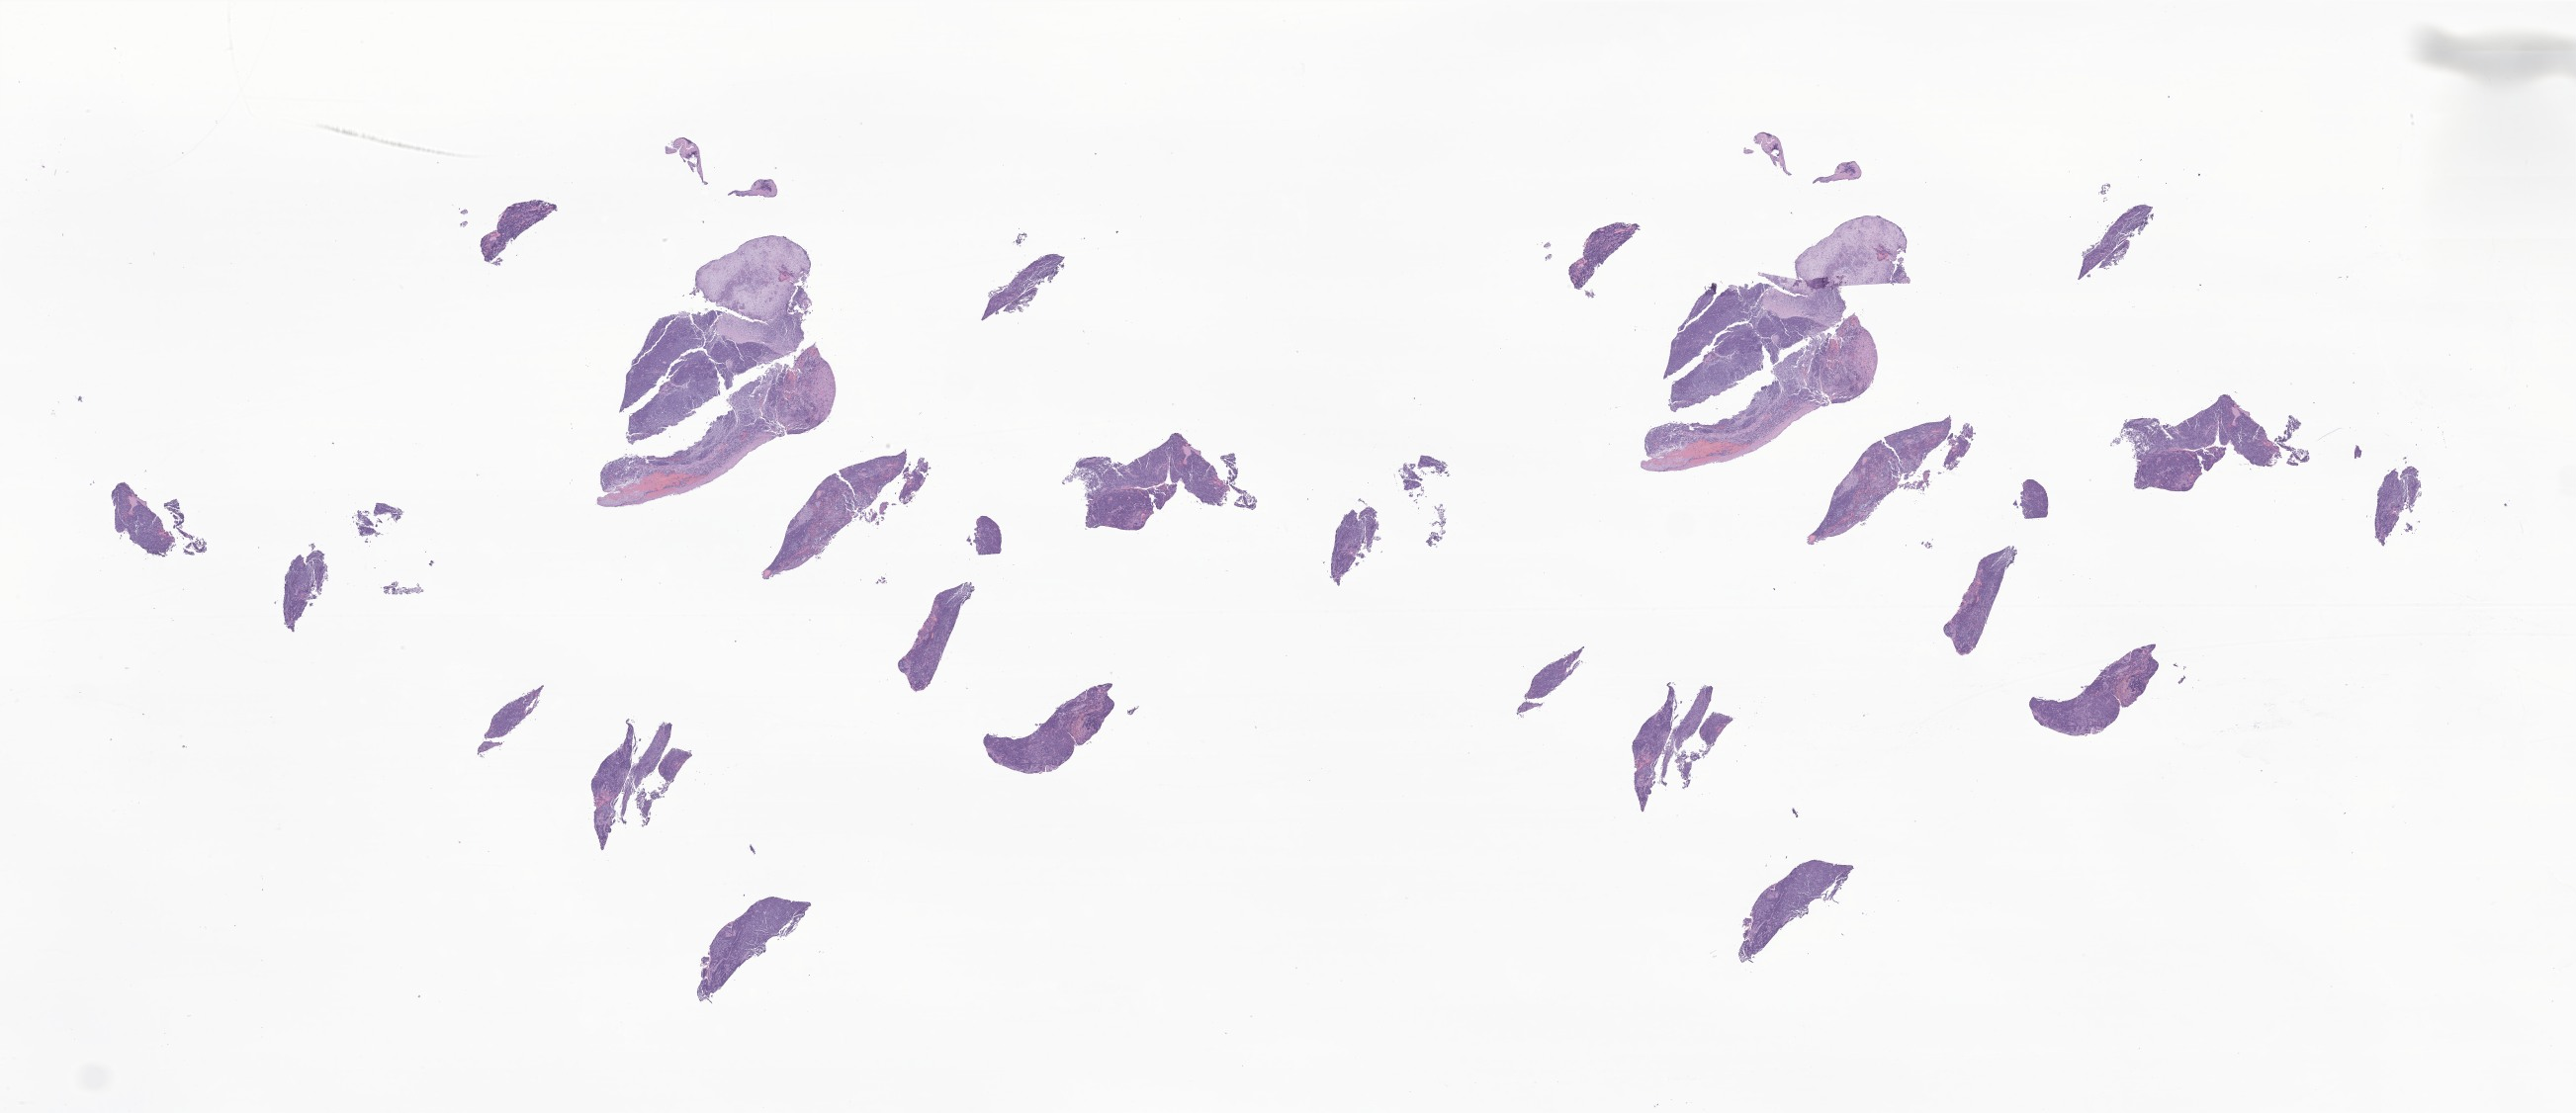
Whole-slide image, H&E stain of tumor tissue from the cerebral ventricle — low-resolution overview of the scanned area, about 43.9 x 19.0 mm. Formalin-fixed paraffin-embedded section. Patient male; age 677 days (about 1.9 years).
Recorded diagnosis: Medulloblastoma, NOS.